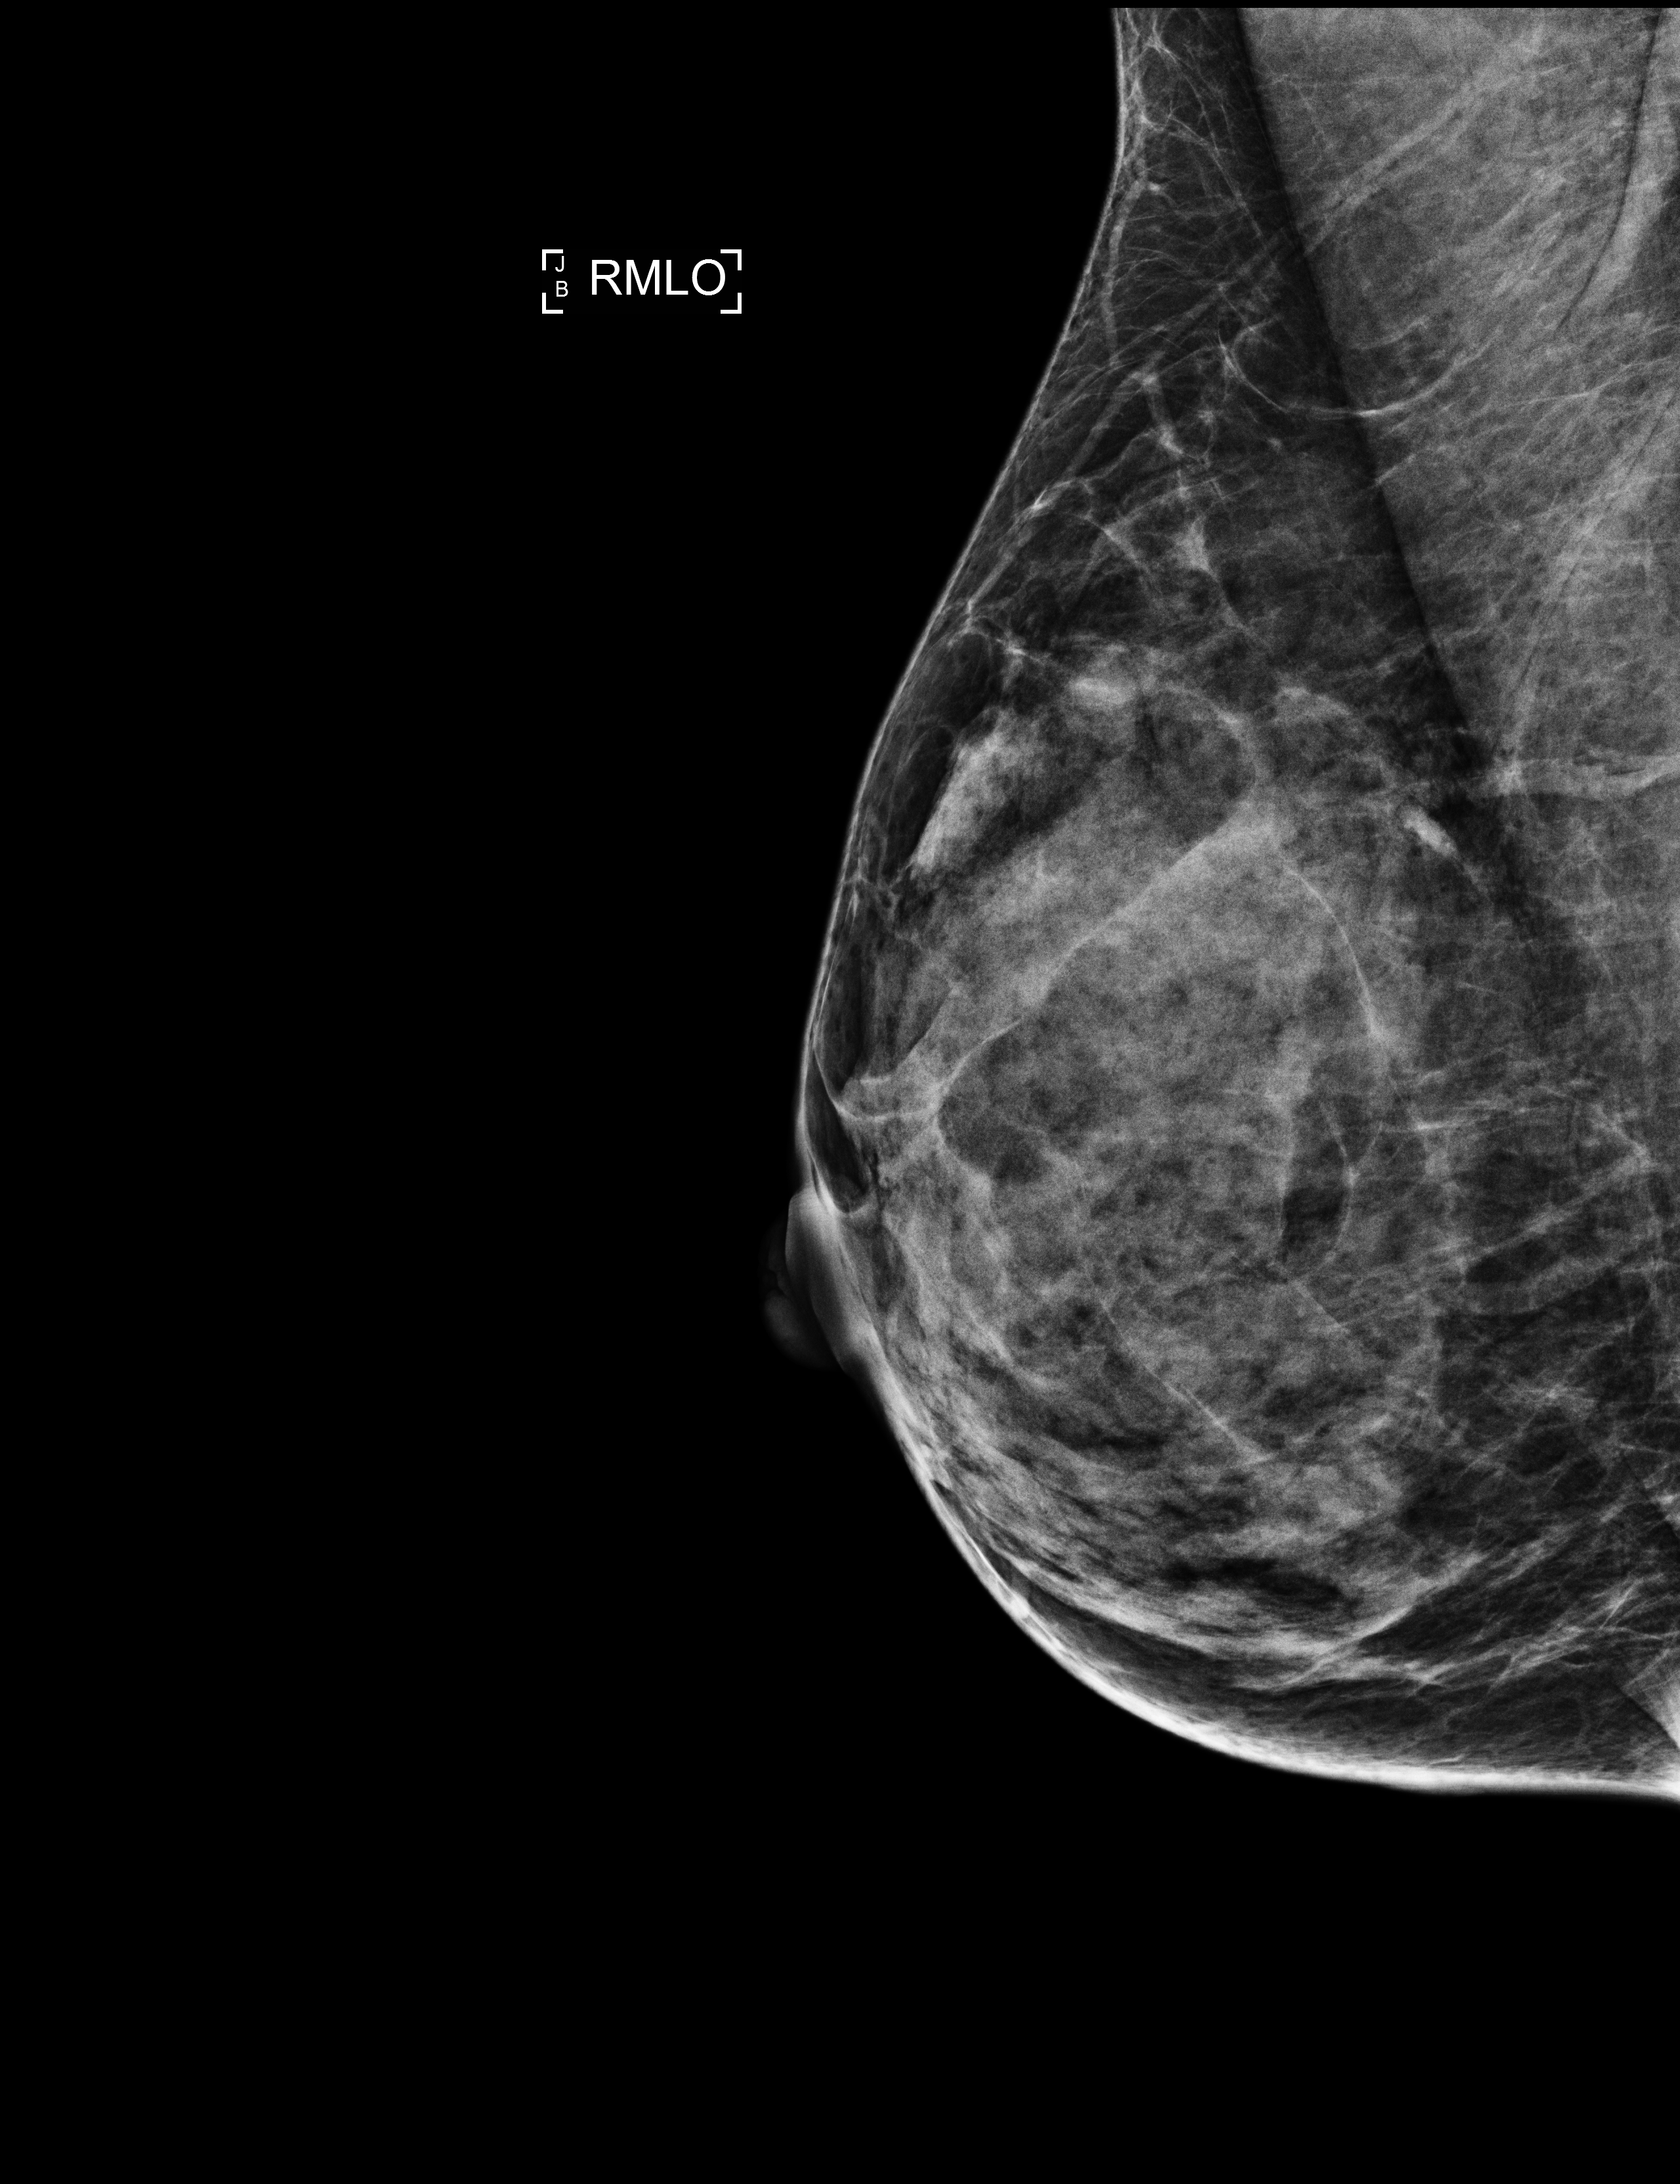
Full-field digital mammogram (FFDM), right breast, medio-lateral oblique projection, screening examination. Patient: female, 46 years.
- breast density at the screening exam (both breasts): extremely dense (BI-RADS density category d)
- final BI-RADS assessment for this screening round (tomosynthesis exam, both breasts): category 1
- recall: no recall after this screen